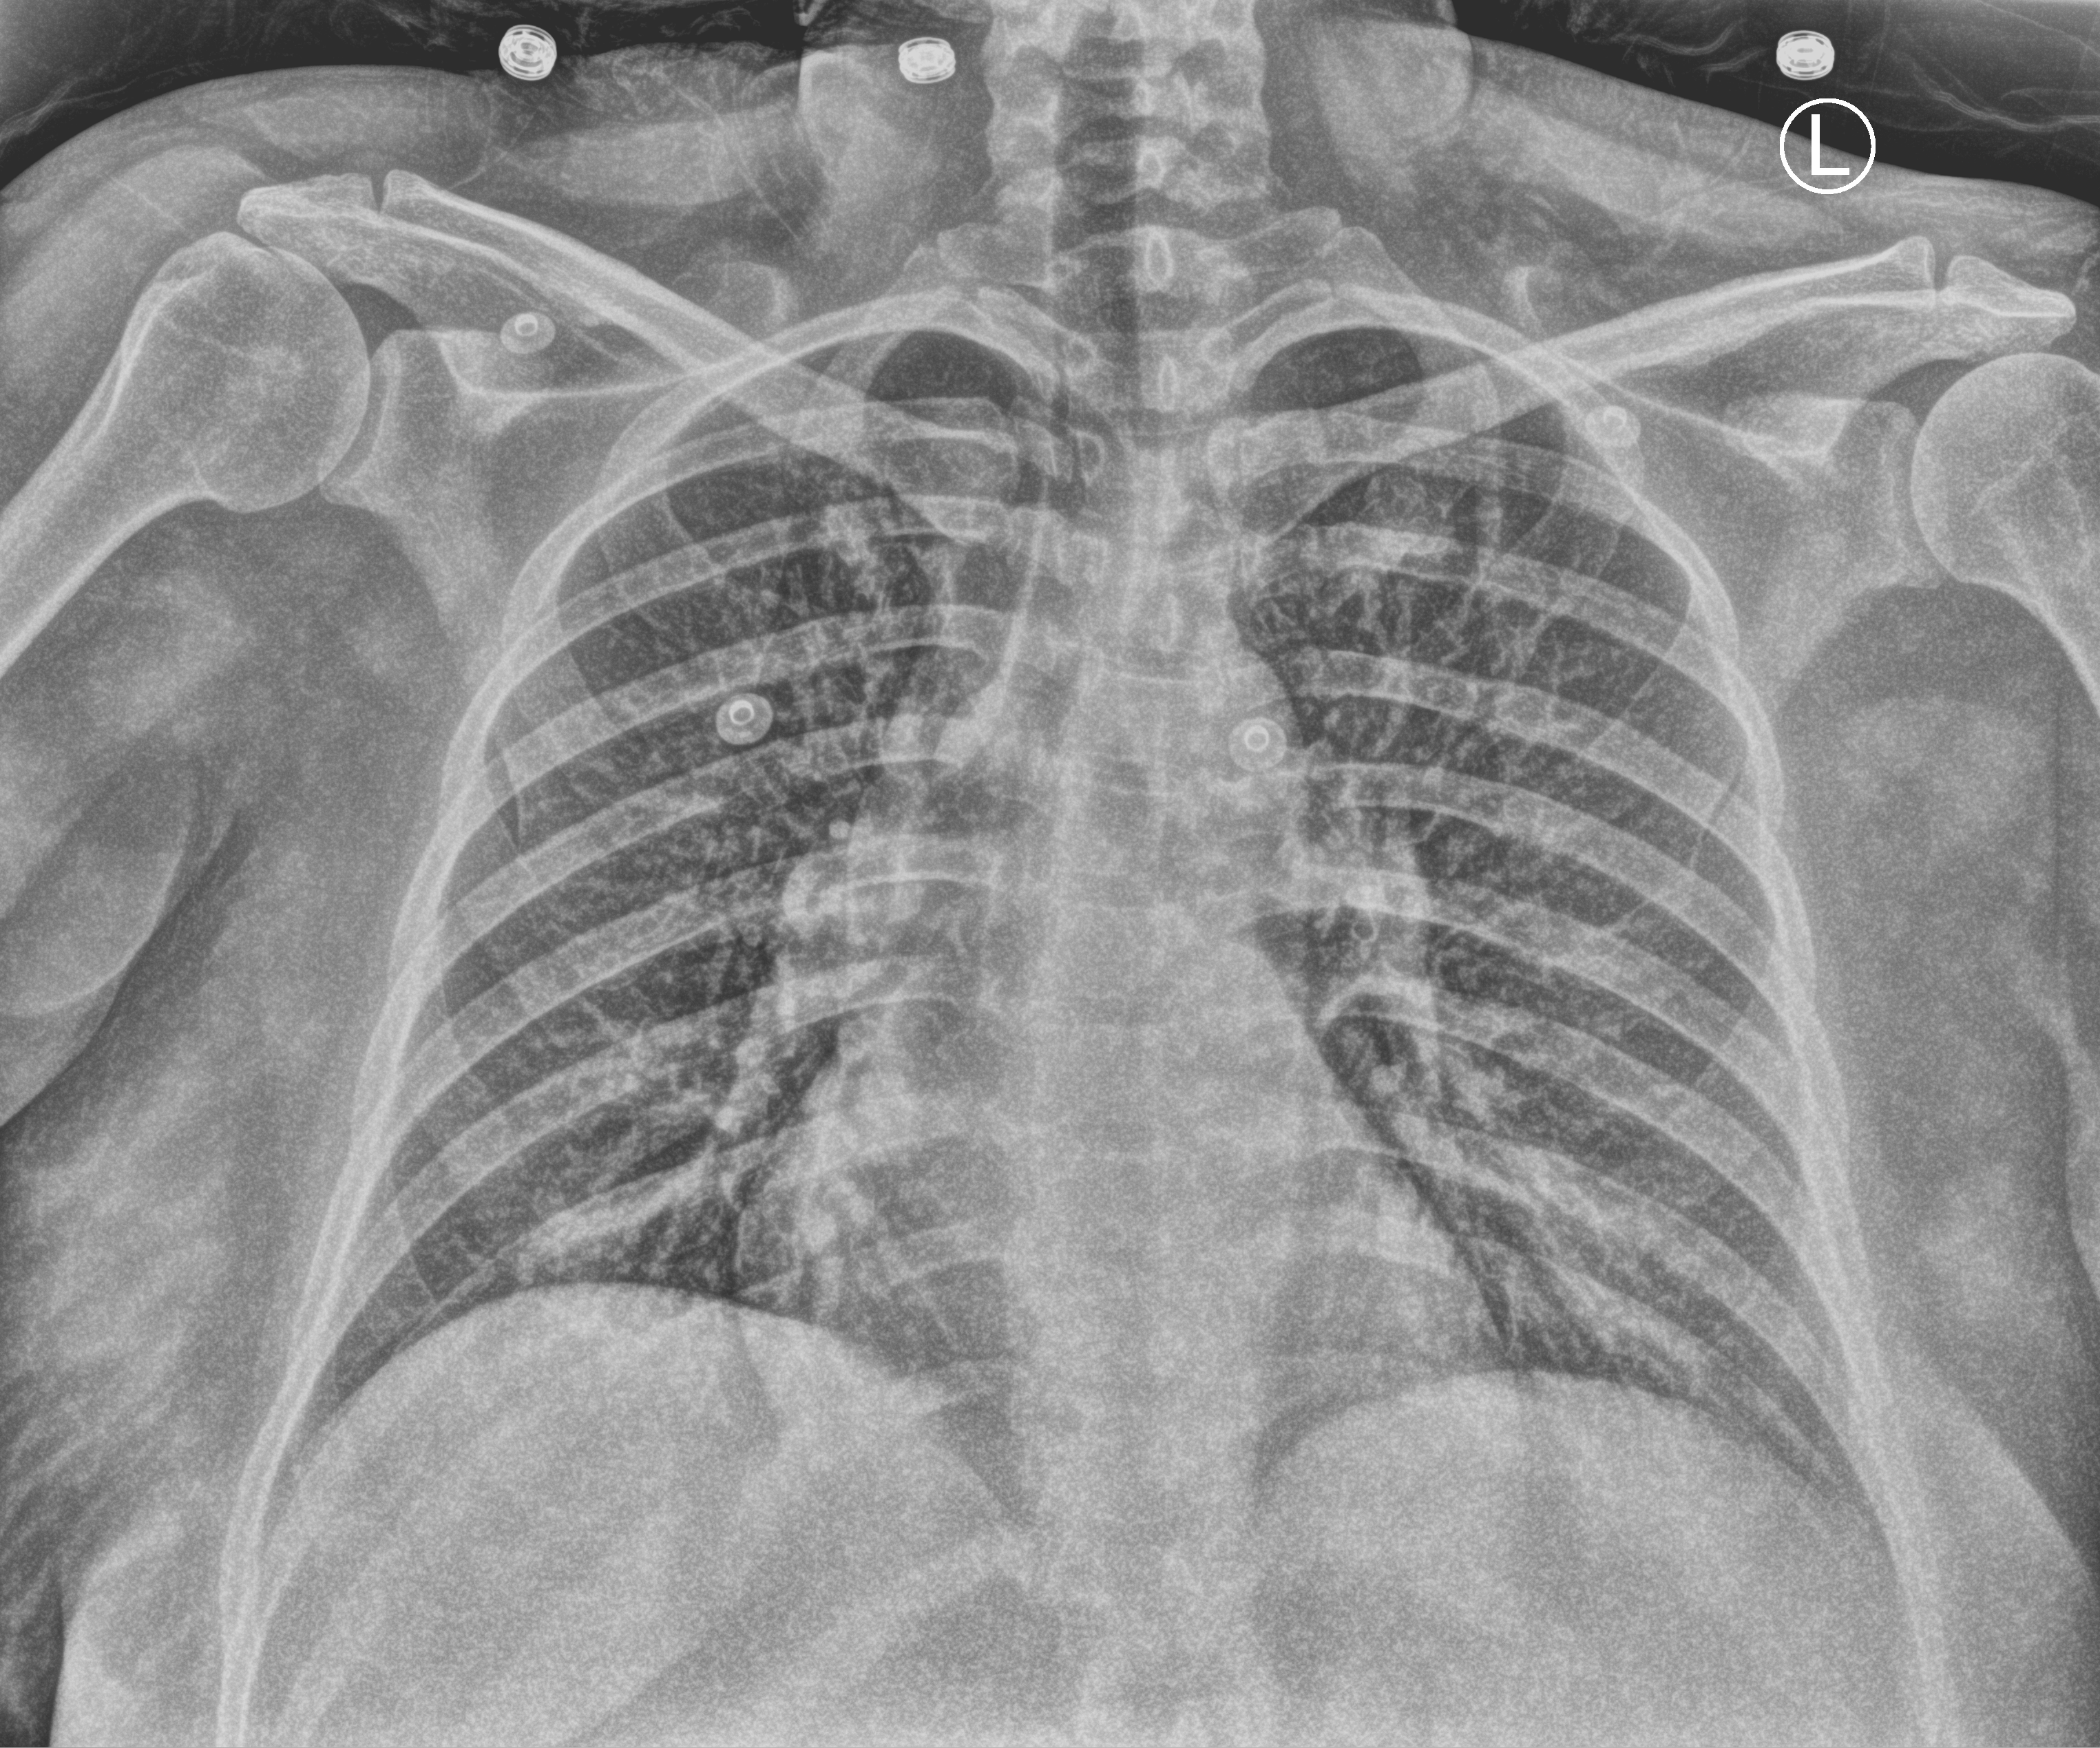
Bedside chest radiograph (computed radiography); anteroposterior (AP) projection. Patient hospitalised with COVID-19; female, aged 18–59 years.
Hospital-stay facts (about this admission, not read from this image; timing relative to this image not recorded): admitted to intensive care during this hospital stay: no.